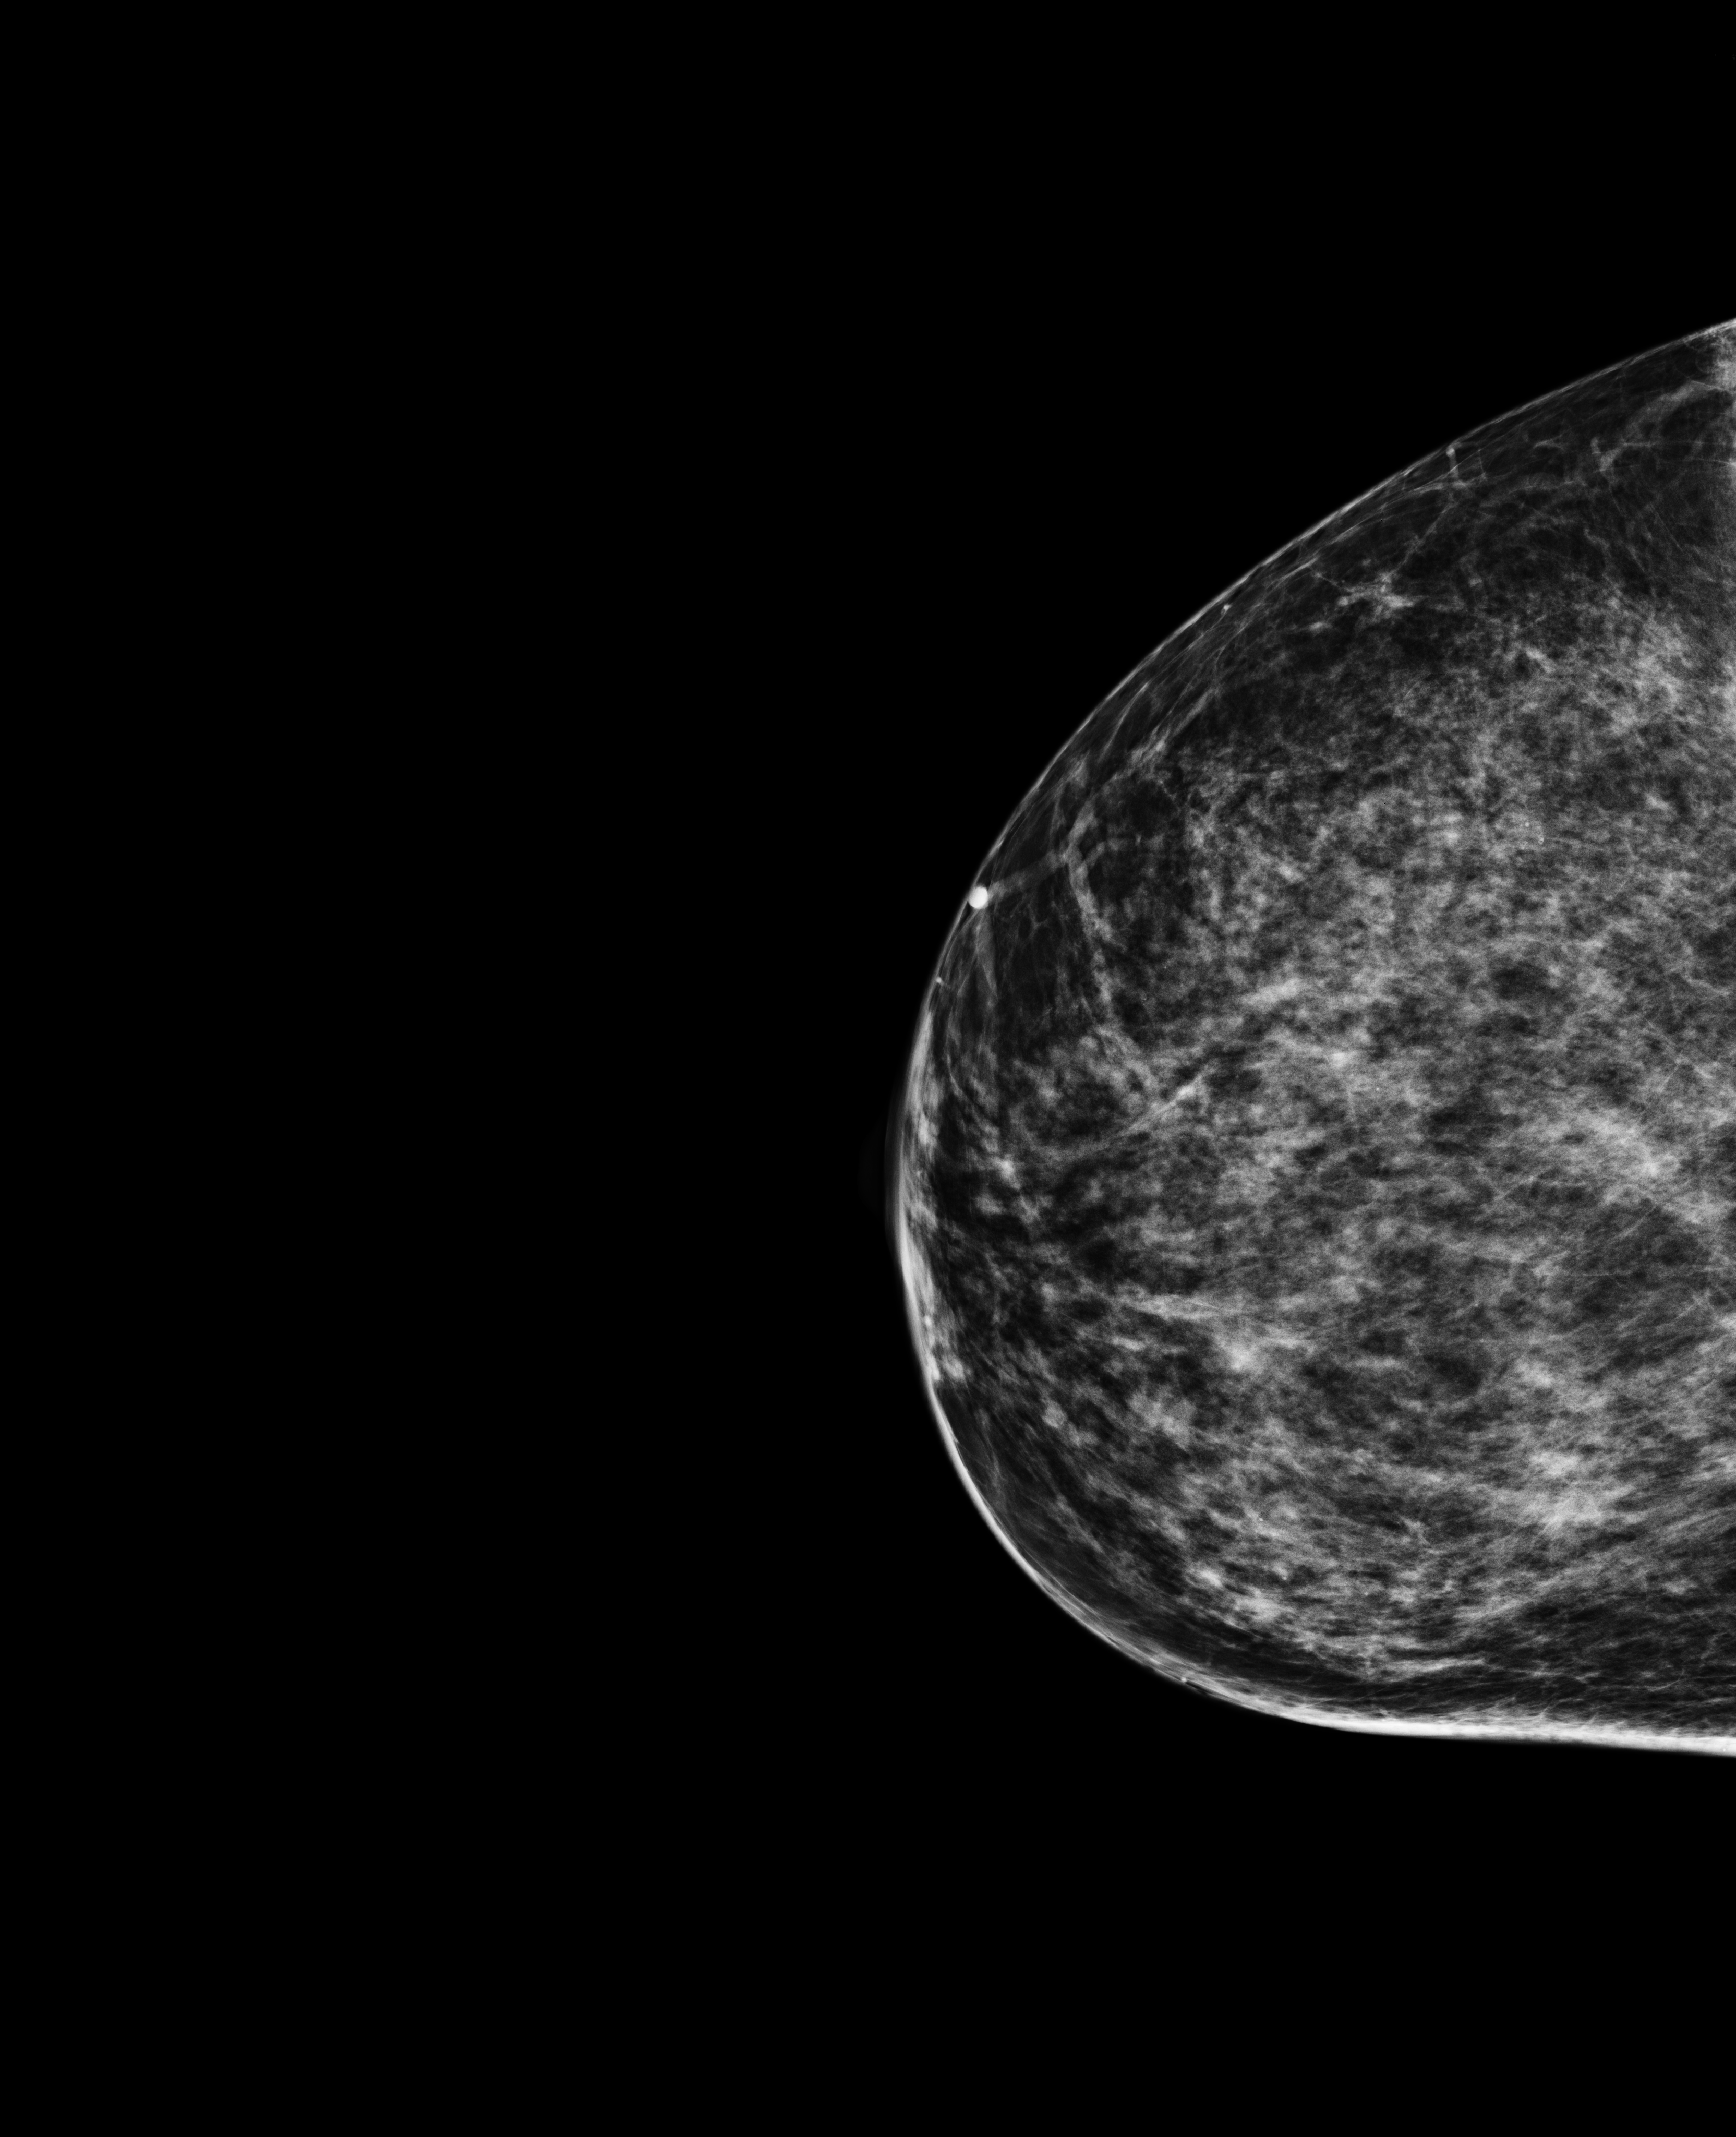
Screening examination. Patient: female, 50 years.
Image type: full-field digital mammogram. Breast: right. Projection: craniocaudal (CC) view. BI-RADS breast density category at the screening exam (both breasts, scale 1–4): 3. Final BI-RADS assessment for this screening round (tomosynthesis exam, both breasts): category 1. Recall: no recall after this screen.